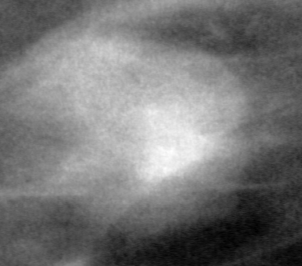
Region of interest cut from a scanned film mammogram (one marked finding), right breast, CC view, BI-RADS breast density category 4 (scale 1–4).
- Mass, shape lobulated, margins ill defined; BI-RADS assessment category 4; subtlety rating 2 on a 1 (subtle) to 5 (obvious) scale; pathology result (as recorded, not read from the image): malignant.